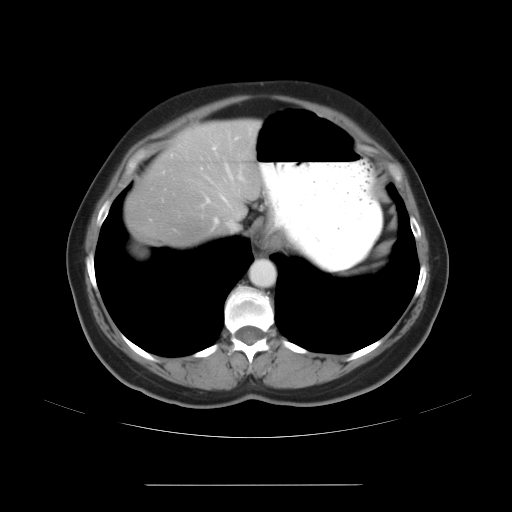
Contrast-enhanced abdominal CT, one axial slice; slice 23 of 27 in the series (ordered by position); reconstruction kernel STANDARD; intravenous contrast given; soft-tissue window (W 400 / L 40 HU); 7.5 mm slice thickness; 512 × 512 image matrix, field of view 440 × 440 mm. Female patient, age 58 years. From the clinical record (not read from this slice): diagnosis: colorectal cancer liver metastases, imaged before liver resection; multiple liver metastases: yes; largest metastasis: 1.9 cm.
Annotated regions visible in this slice (expert manual segmentation):
- hepatic veins: bounding box [x1, y1, x2, y2] px = [213, 164, 243, 228]
- liver: [129, 121, 261, 245]
- planned liver remnant (the part of the liver to remain after resection): [130, 121, 261, 227]
- portal vein (with intrahepatic branches): [163, 144, 218, 202]